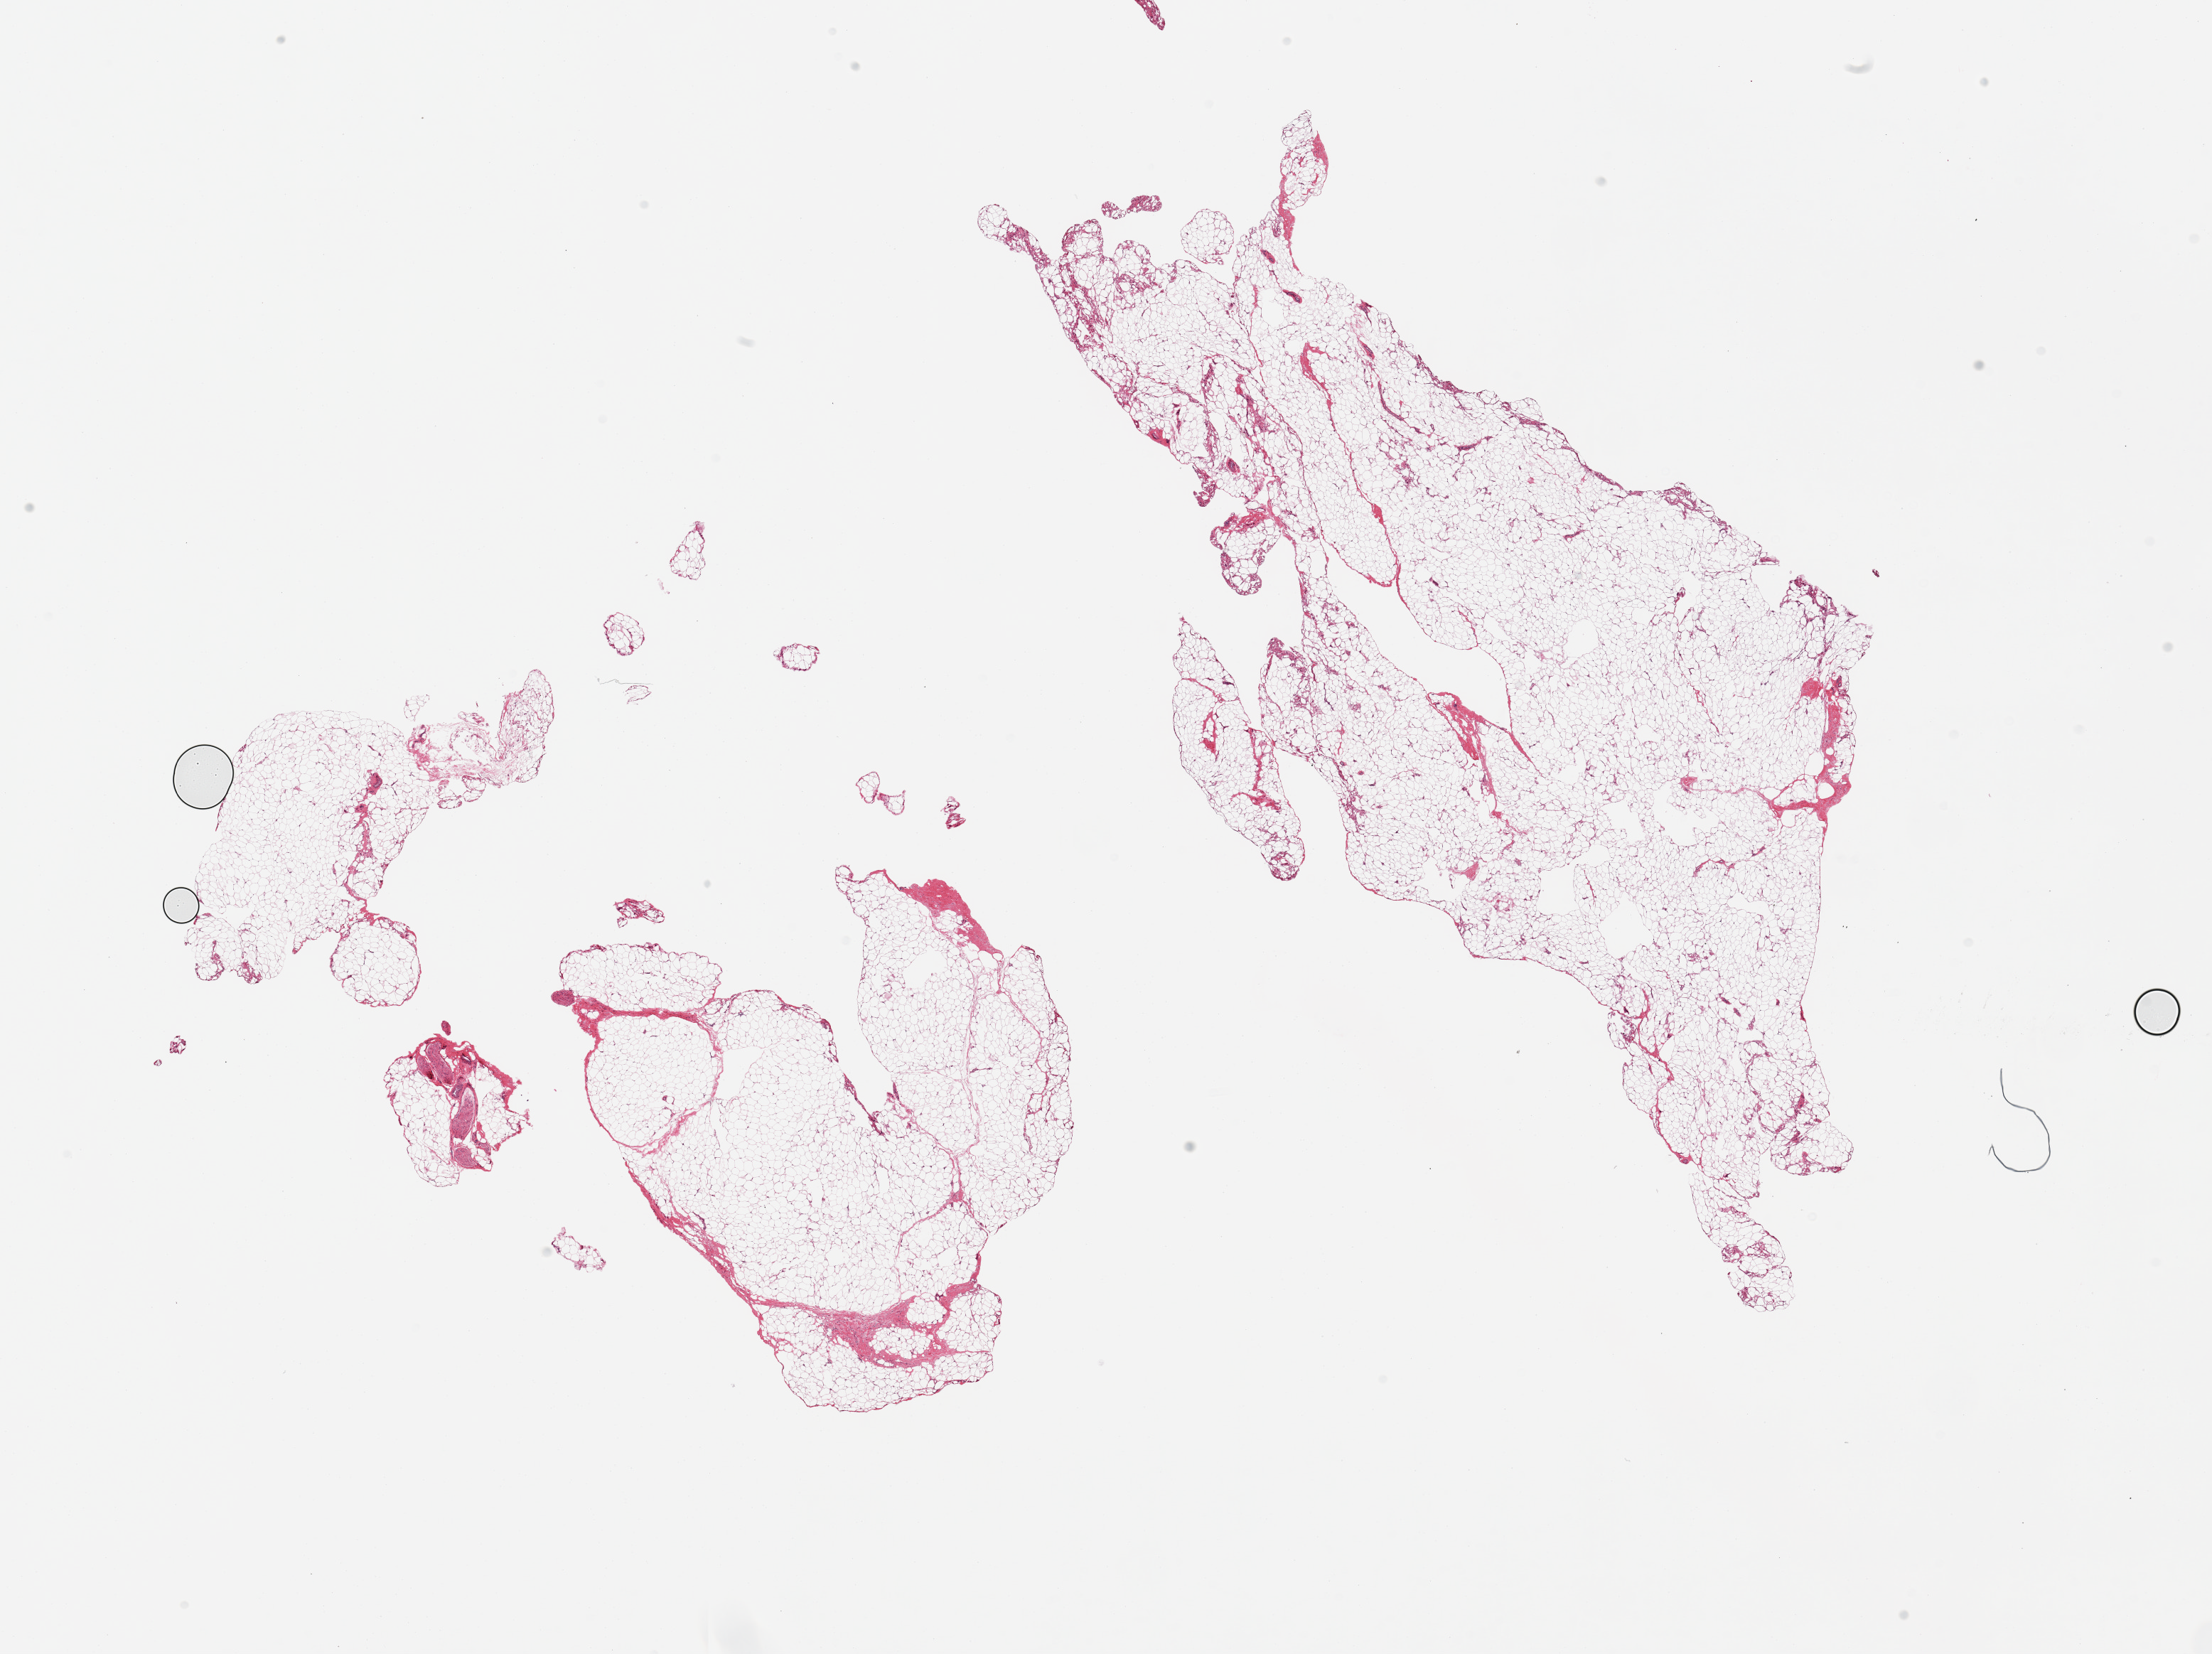
Digitized hematoxylin and eosin (H&E)-stained section, shown as a low-resolution overview of the whole scanned area (about 24.6 x 18.4 mm); PAXgene-fixed, paraffin-embedded tissue; sampled site (target tissue): adipose tissue; donor tissue sample. Female donor.
• review note (as recorded): 2 pieces; small attachment of nerve